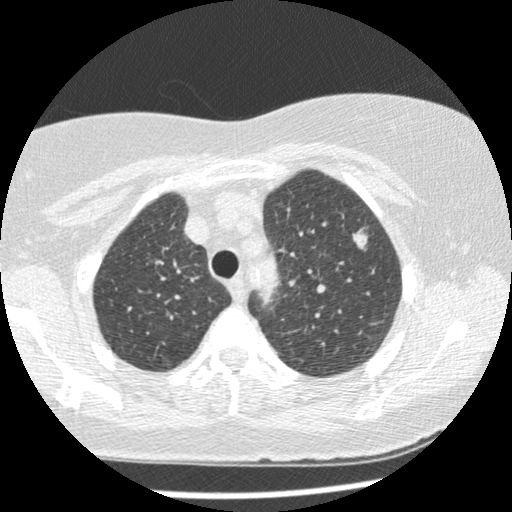
Low-dose screening chest CT, one axial slice; slice 184 of 241 in the series (ordered by position); reconstruction kernel STANDARD; 120 kVp; lung window (W 1500 / L -600 HU); 1.25 mm slice thickness; 512 × 512 image matrix.
Structures marked on this image (expert manual segmentation):
- lesion 2 (tumor, upper lobe of left lung): bounding box (x1, y1, x2, y2) in pixels: (352, 227, 368, 251)